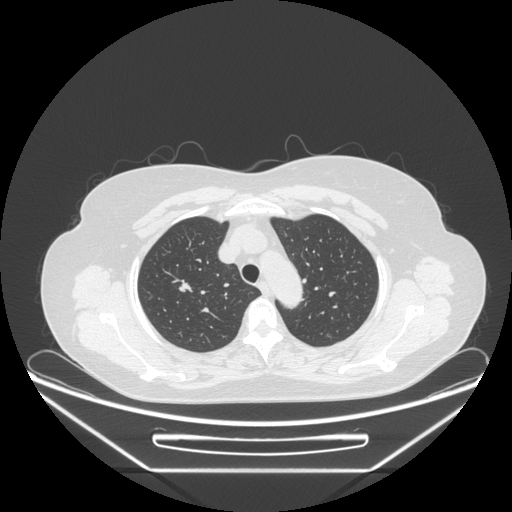
Chest CT, one axial slice; position 193 of 236 along the scan axis; reconstruction kernel STANDARD; lung window (W 1500 / L -600 HU); 1.25 mm slice thickness; 512 × 512 image matrix, field of view 433 × 433 mm. Patient: female, 60 years. From the clinical record (not read from this slice): clinical TNM (as recorded): T1c N0 M0; histopathological grade: G2-3.
Annotated regions visible in this slice (bounding box drawn by a radiologist):
- lung tumour (recorded histology: adenocarcinoma): box from (x=172, y=274) to (x=201, y=303) px